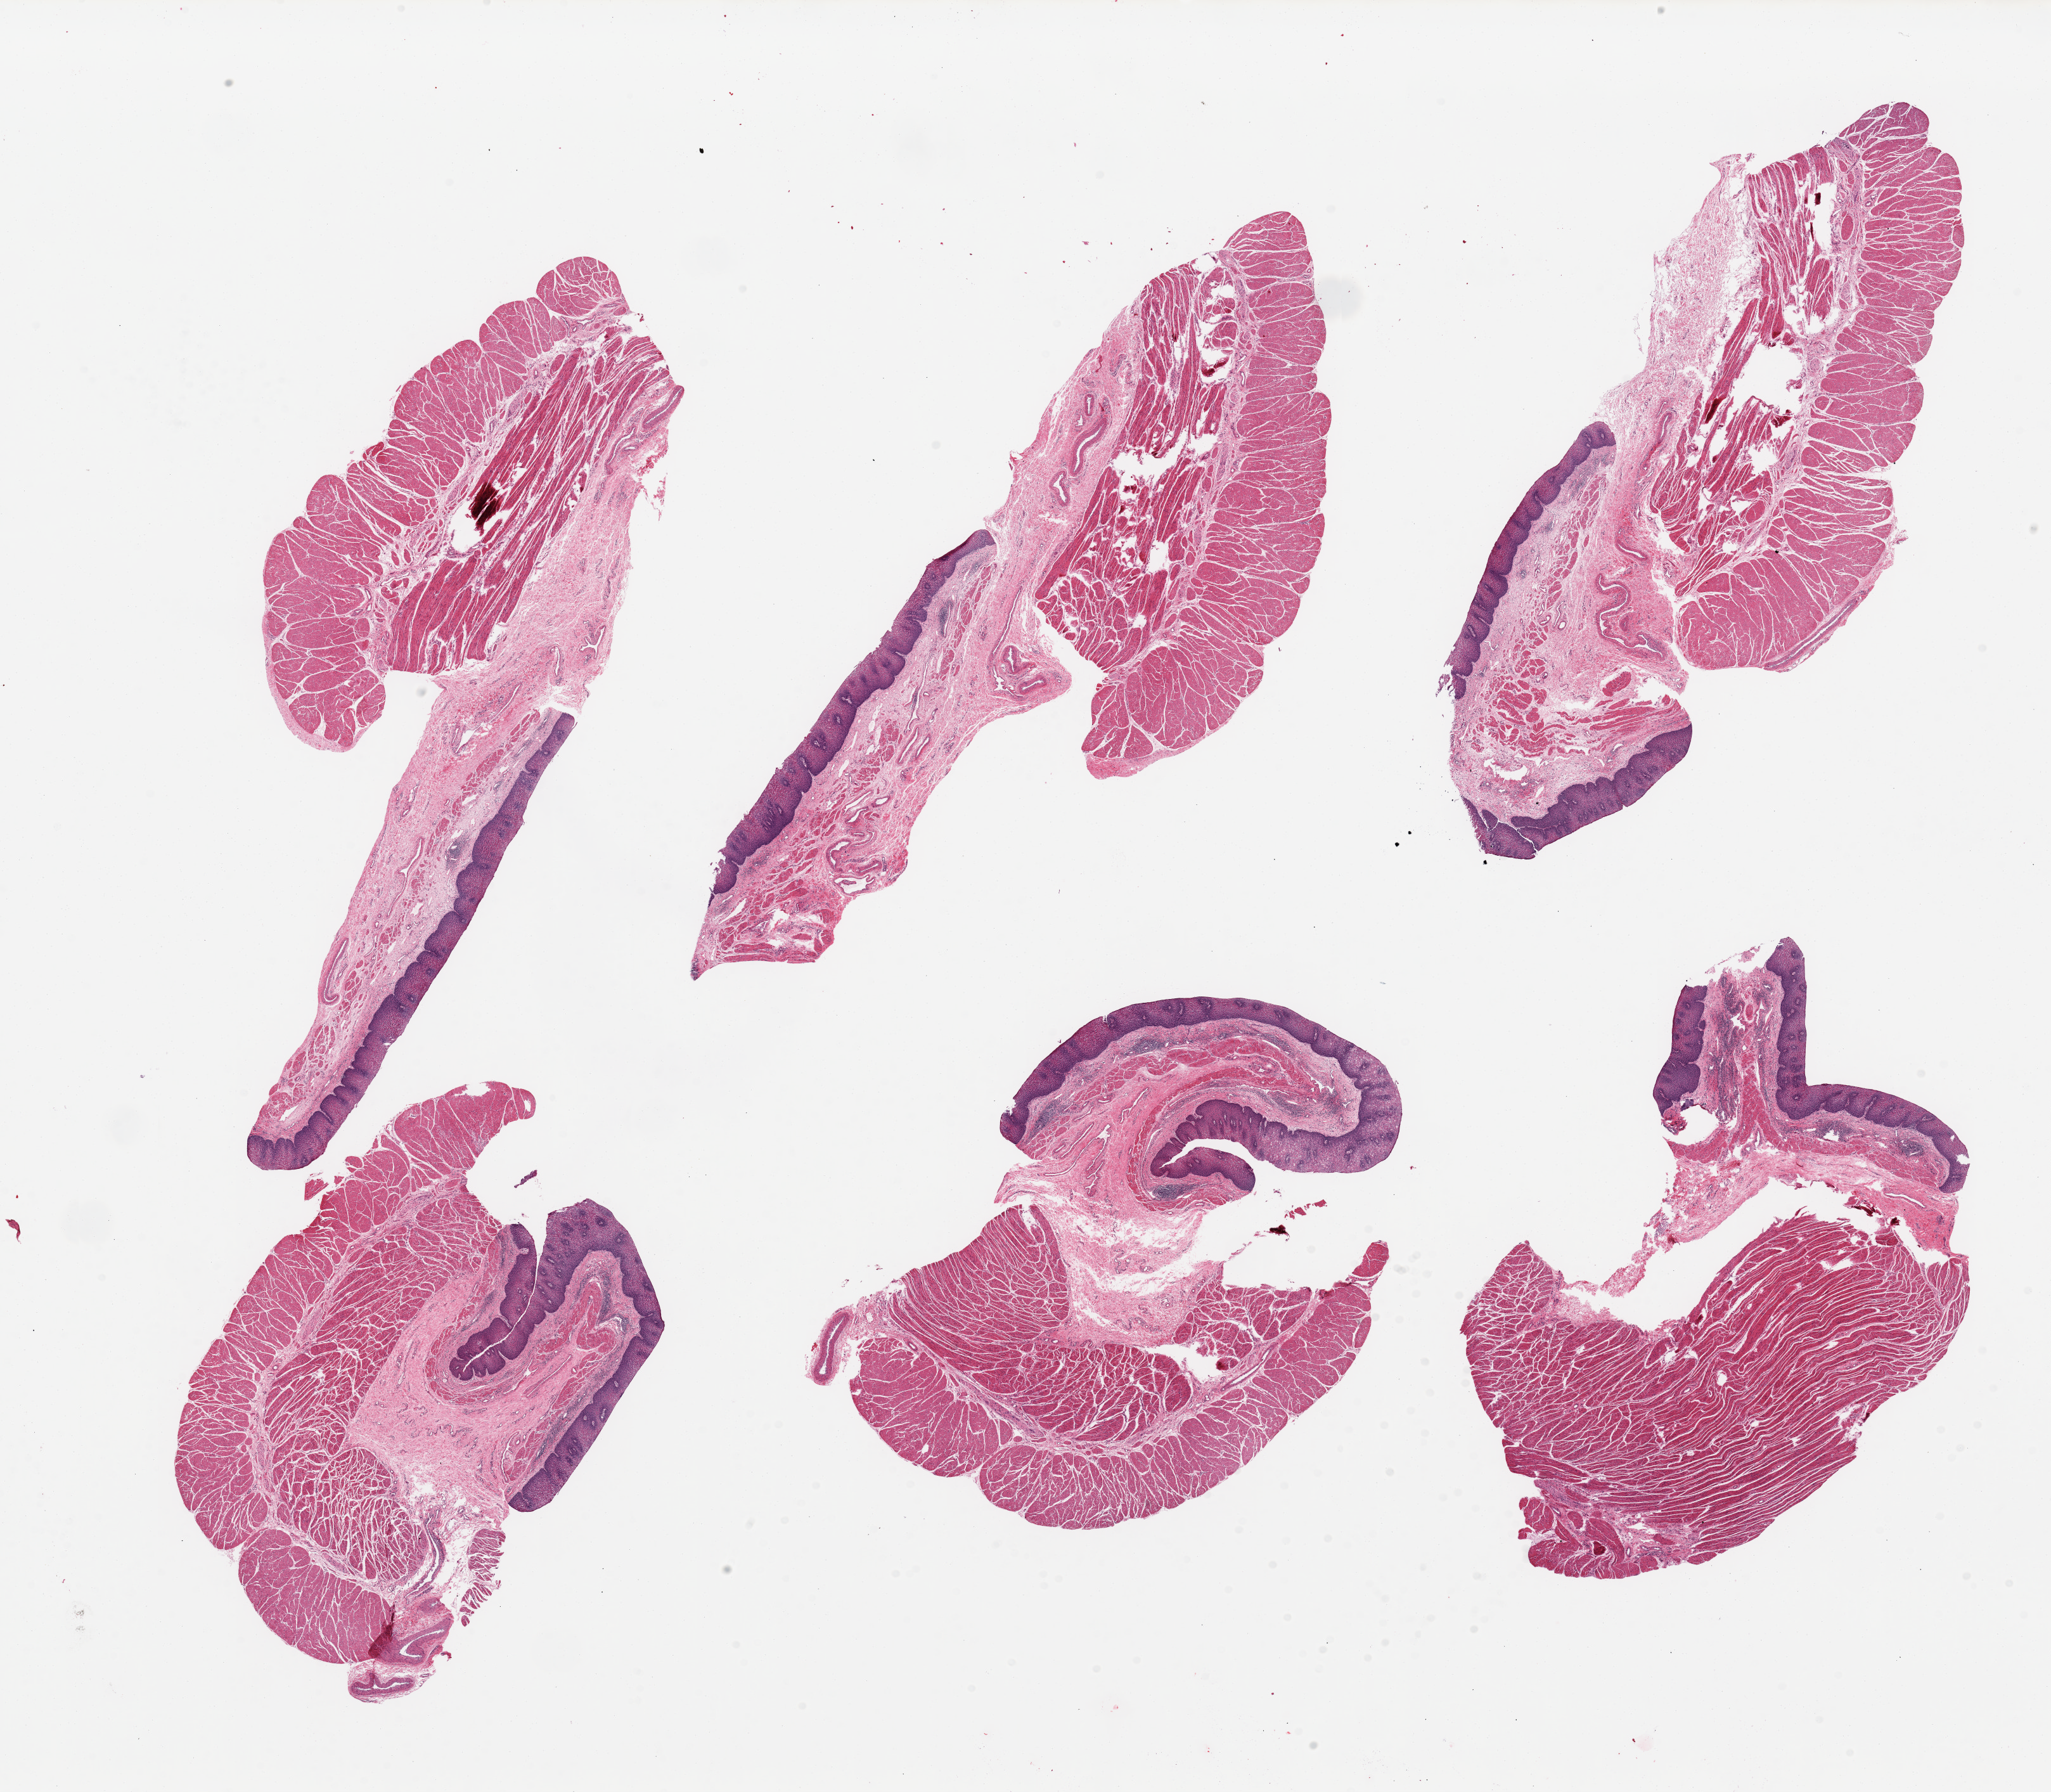
Haematoxylin and eosin whole-slide image — shown as a low-resolution overview of the whole scanned area (about 25.6 x 22.4 mm). PAXgene-fixed paraffin-embedded (PFPE) section. Sampled site (target tissue): esophageal muscle. Tissue donor sample.
• reviewer comment on this tissue sample: 6 pieces; all with both mucosa & muscularis propria